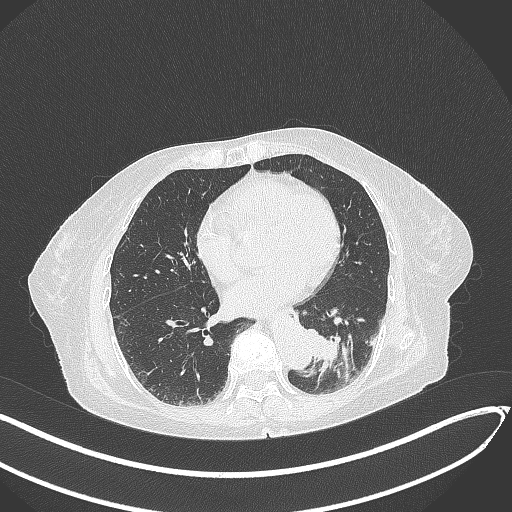
Chest CT, one axial slice. Position 94 of 324 along the scan axis. Reconstruction kernel B70f. 120 kVp. Lung window (W 1500 / L -600 HU). 1 mm slice thickness. 512 × 512 image matrix, field of view 400 × 400 mm. Patient: female, 82 years. Case-level facts recorded for this patient, not image findings: clinical TNM (as recorded): T1b N0 M1.
Annotated regions visible in this slice (rectangle marked by the reading radiologist):
- lung tumour (recorded histology: adenocarcinoma): bounding box (x1, y1, x2, y2) in pixels: (305, 326, 348, 375)